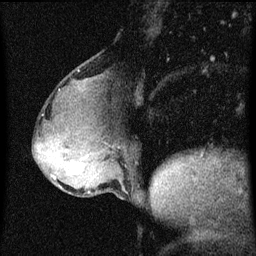
Breast MRI (dynamic contrast-enhanced), one sagittal slice; slice 25 of 60 in the series (ordered by position); dynamic contrast-enhanced series, image 2 of 3 at this slice position (ordered by acquisition); 1.5 T; TE 4.2 ms, TR 8 ms; 2 mm slice thickness; 256 × 256 image matrix. Patient: female, 49 years.
Structures marked on this image (semi-automatic segmentation, software-assisted and operator-edited):
- analysis volume of interest (the breast-tissue region the enhancement analysis was run in; not a lesion): bounding box <51,158,96,185> (left, top, right, bottom; pixels)
- tumour enhancement mask (voxels above the 70 % enhancement threshold inside the analysis volume of interest): <72,164,84,175>